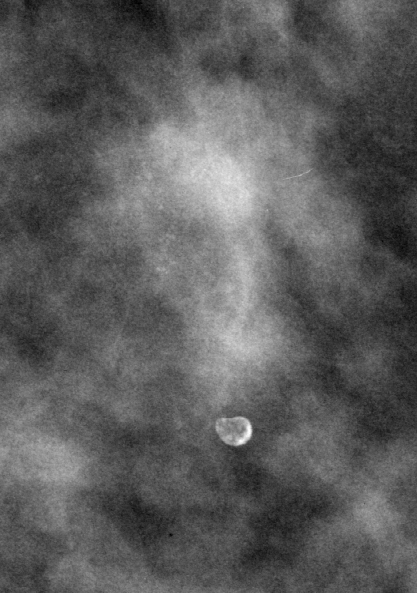
Crop from a digitized film mammogram around one marked abnormality, left breast, CC view.
- Calcifications, morphology punctate, distribution clustered; BI-RADS assessment category 3; pathology result (as recorded, not read from the image): benign.